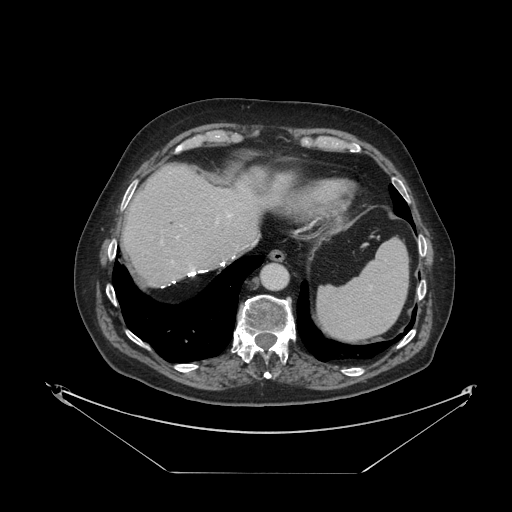
Contrast-enhanced abdominal CT, one axial slice. Position 98 of 121 along the scan axis. 120 kVp. Intravenous contrast given. Soft-tissue window (W 400 / L 40 HU). 512 × 512 image matrix. Male patient, age 68 years. Case-level facts recorded for this patient, not image findings: diagnosis: colorectal cancer liver metastases, imaged before liver resection; multiple liver metastases: no; largest metastasis: 4 cm; chemotherapy before resection: yes.
Annotated regions visible in this slice (expert manual segmentation):
- hepatic veins: bounding box (x1, y1, x2, y2) in pixels: (177, 214, 233, 237)
- liver: (123, 165, 290, 285)
- planned liver remnant (the part of the liver to remain after resection): (123, 165, 290, 285)
- portal vein (with intrahepatic branches): (161, 220, 219, 263)